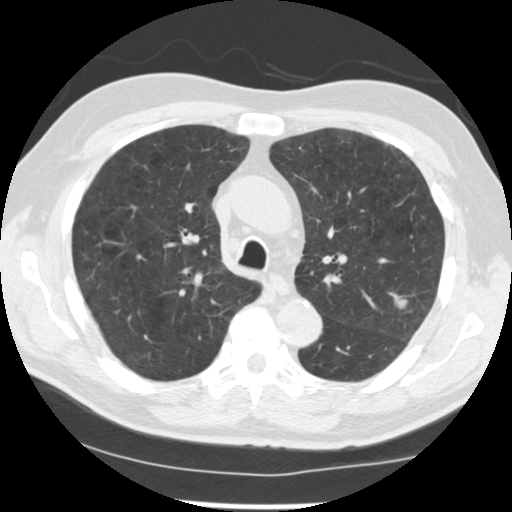
Low-dose screening chest CT, one axial slice; position 168 of 249 along the scan axis; 120 kVp; lung window (W 1500 / L -600 HU); 2.5 mm slice thickness; 512 × 512 image matrix, field of view 341 × 341 mm.
Annotated regions visible in this slice (manually delineated by an expert):
- lesion 1 (tumor, upper lobe of left lung): bounding box <396,299,407,308> (left, top, right, bottom; pixels)